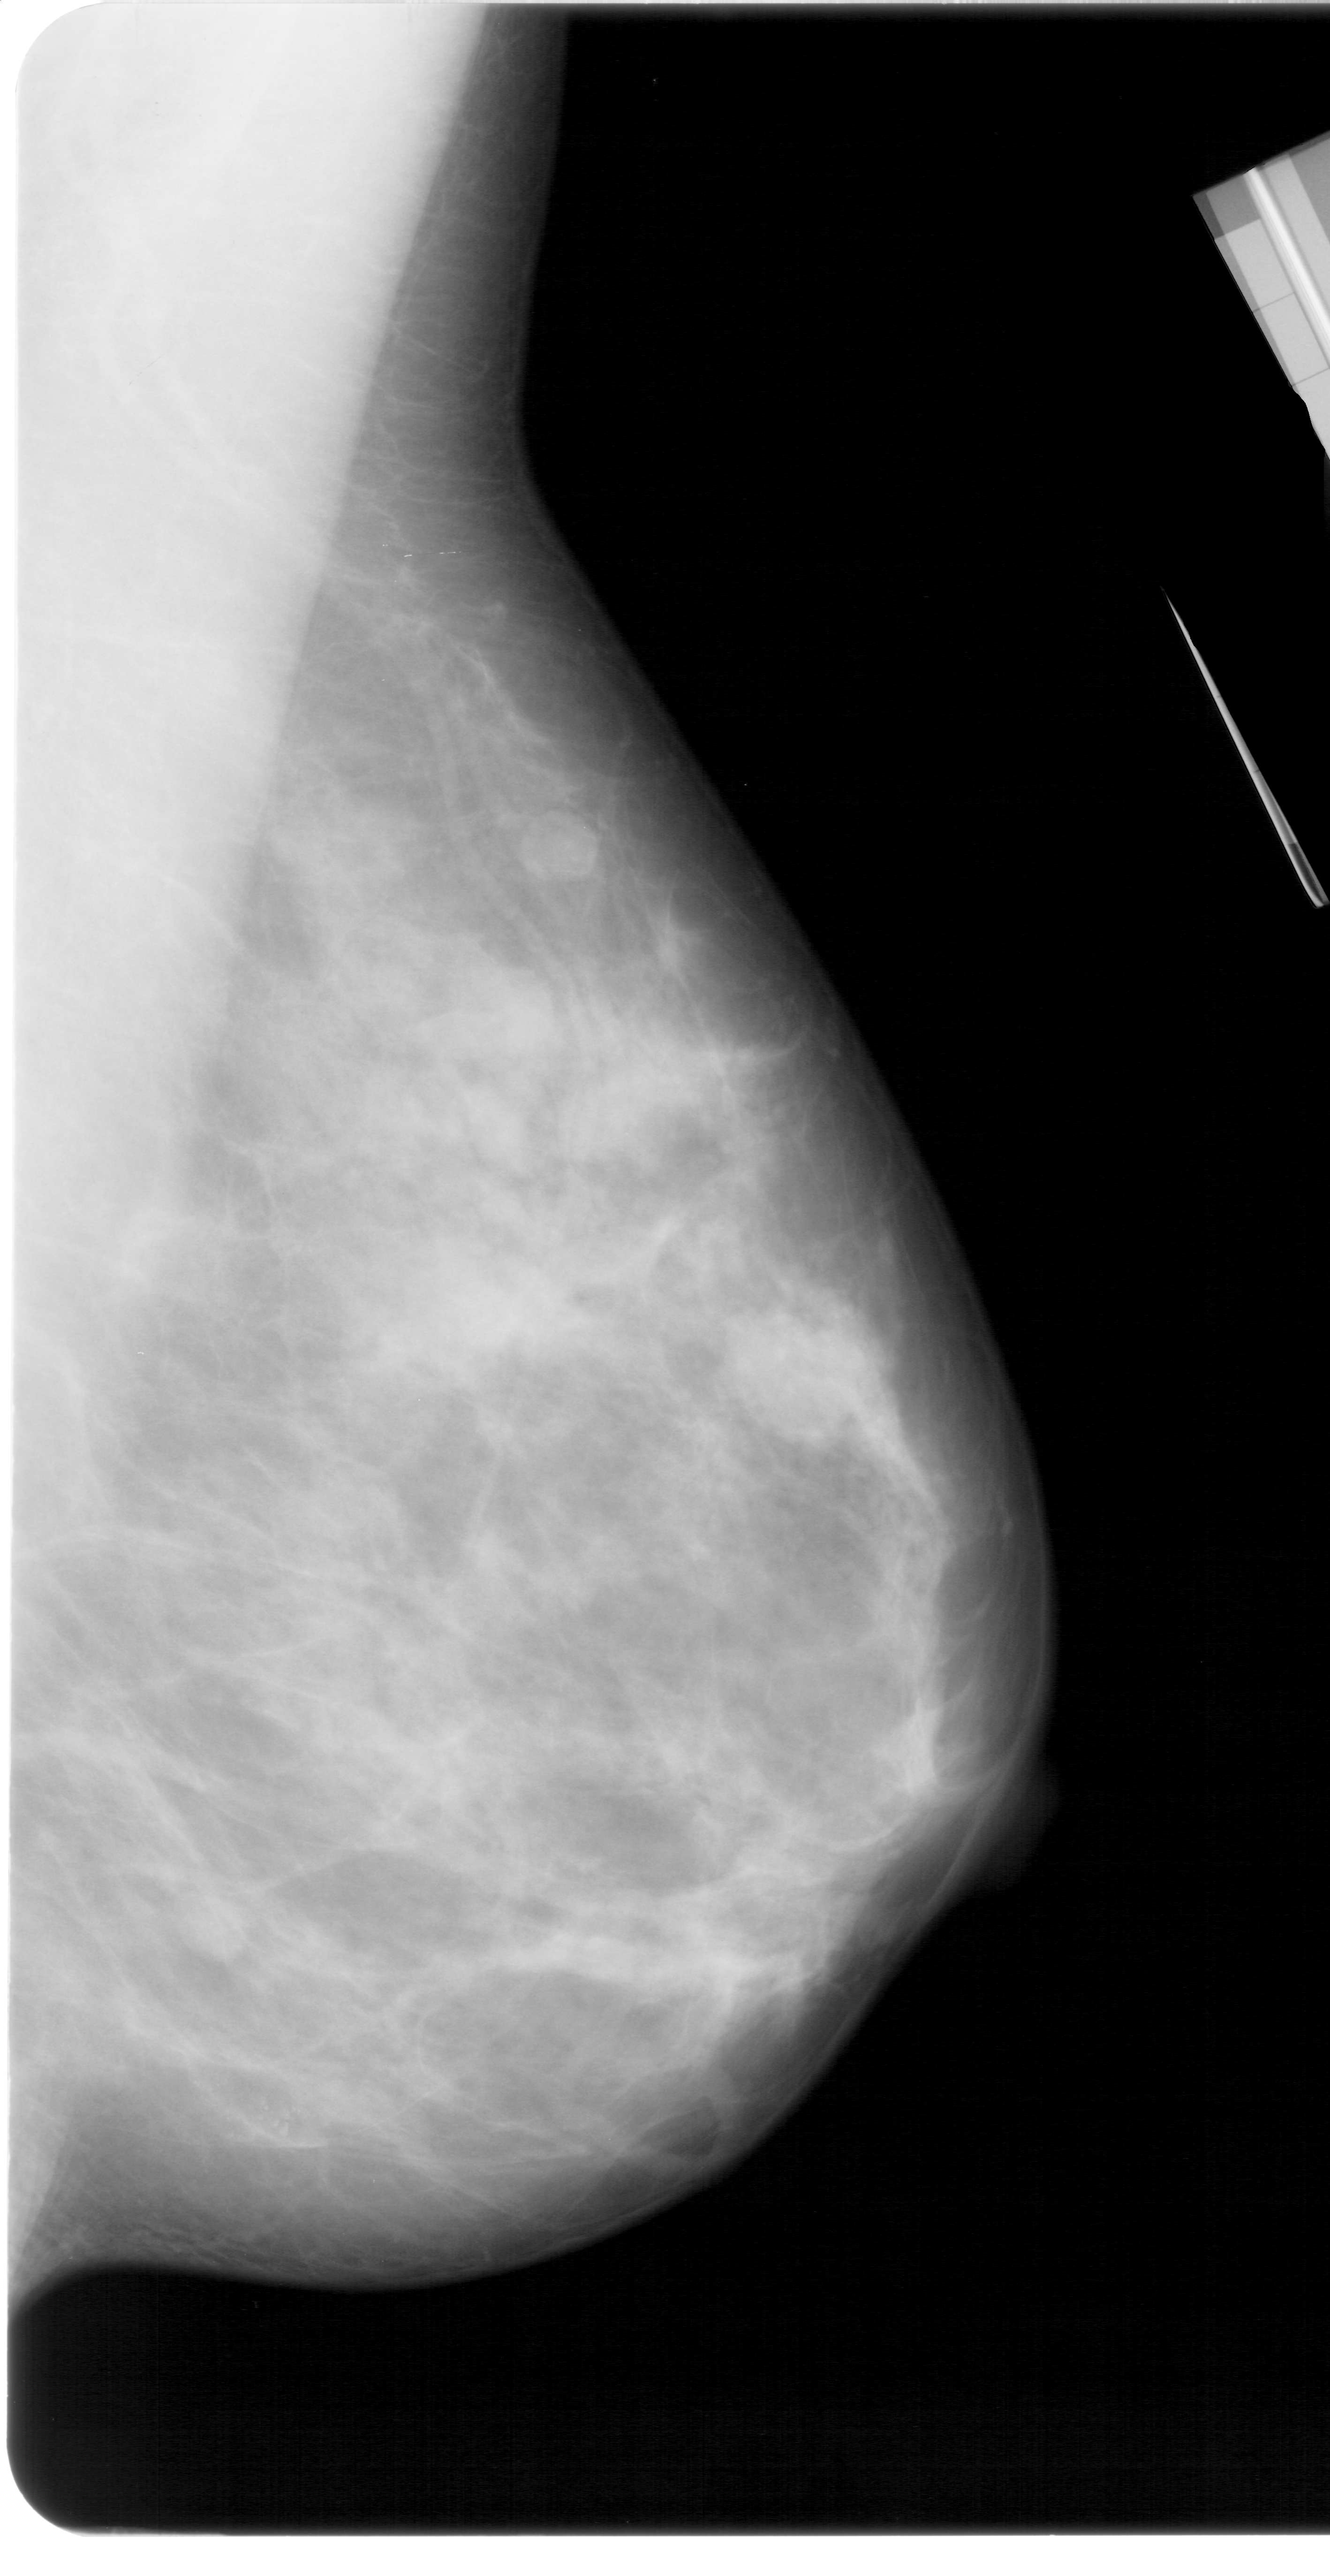
Digitized screen-film mammogram, right breast, MLO view, breast composition: extremely dense (BI-RADS density category 4 of 4).
Calcifications, morphology pleomorphic, distribution clustered; BI-RADS assessment category 4; pathology result (as recorded, not read from the image): malignant.